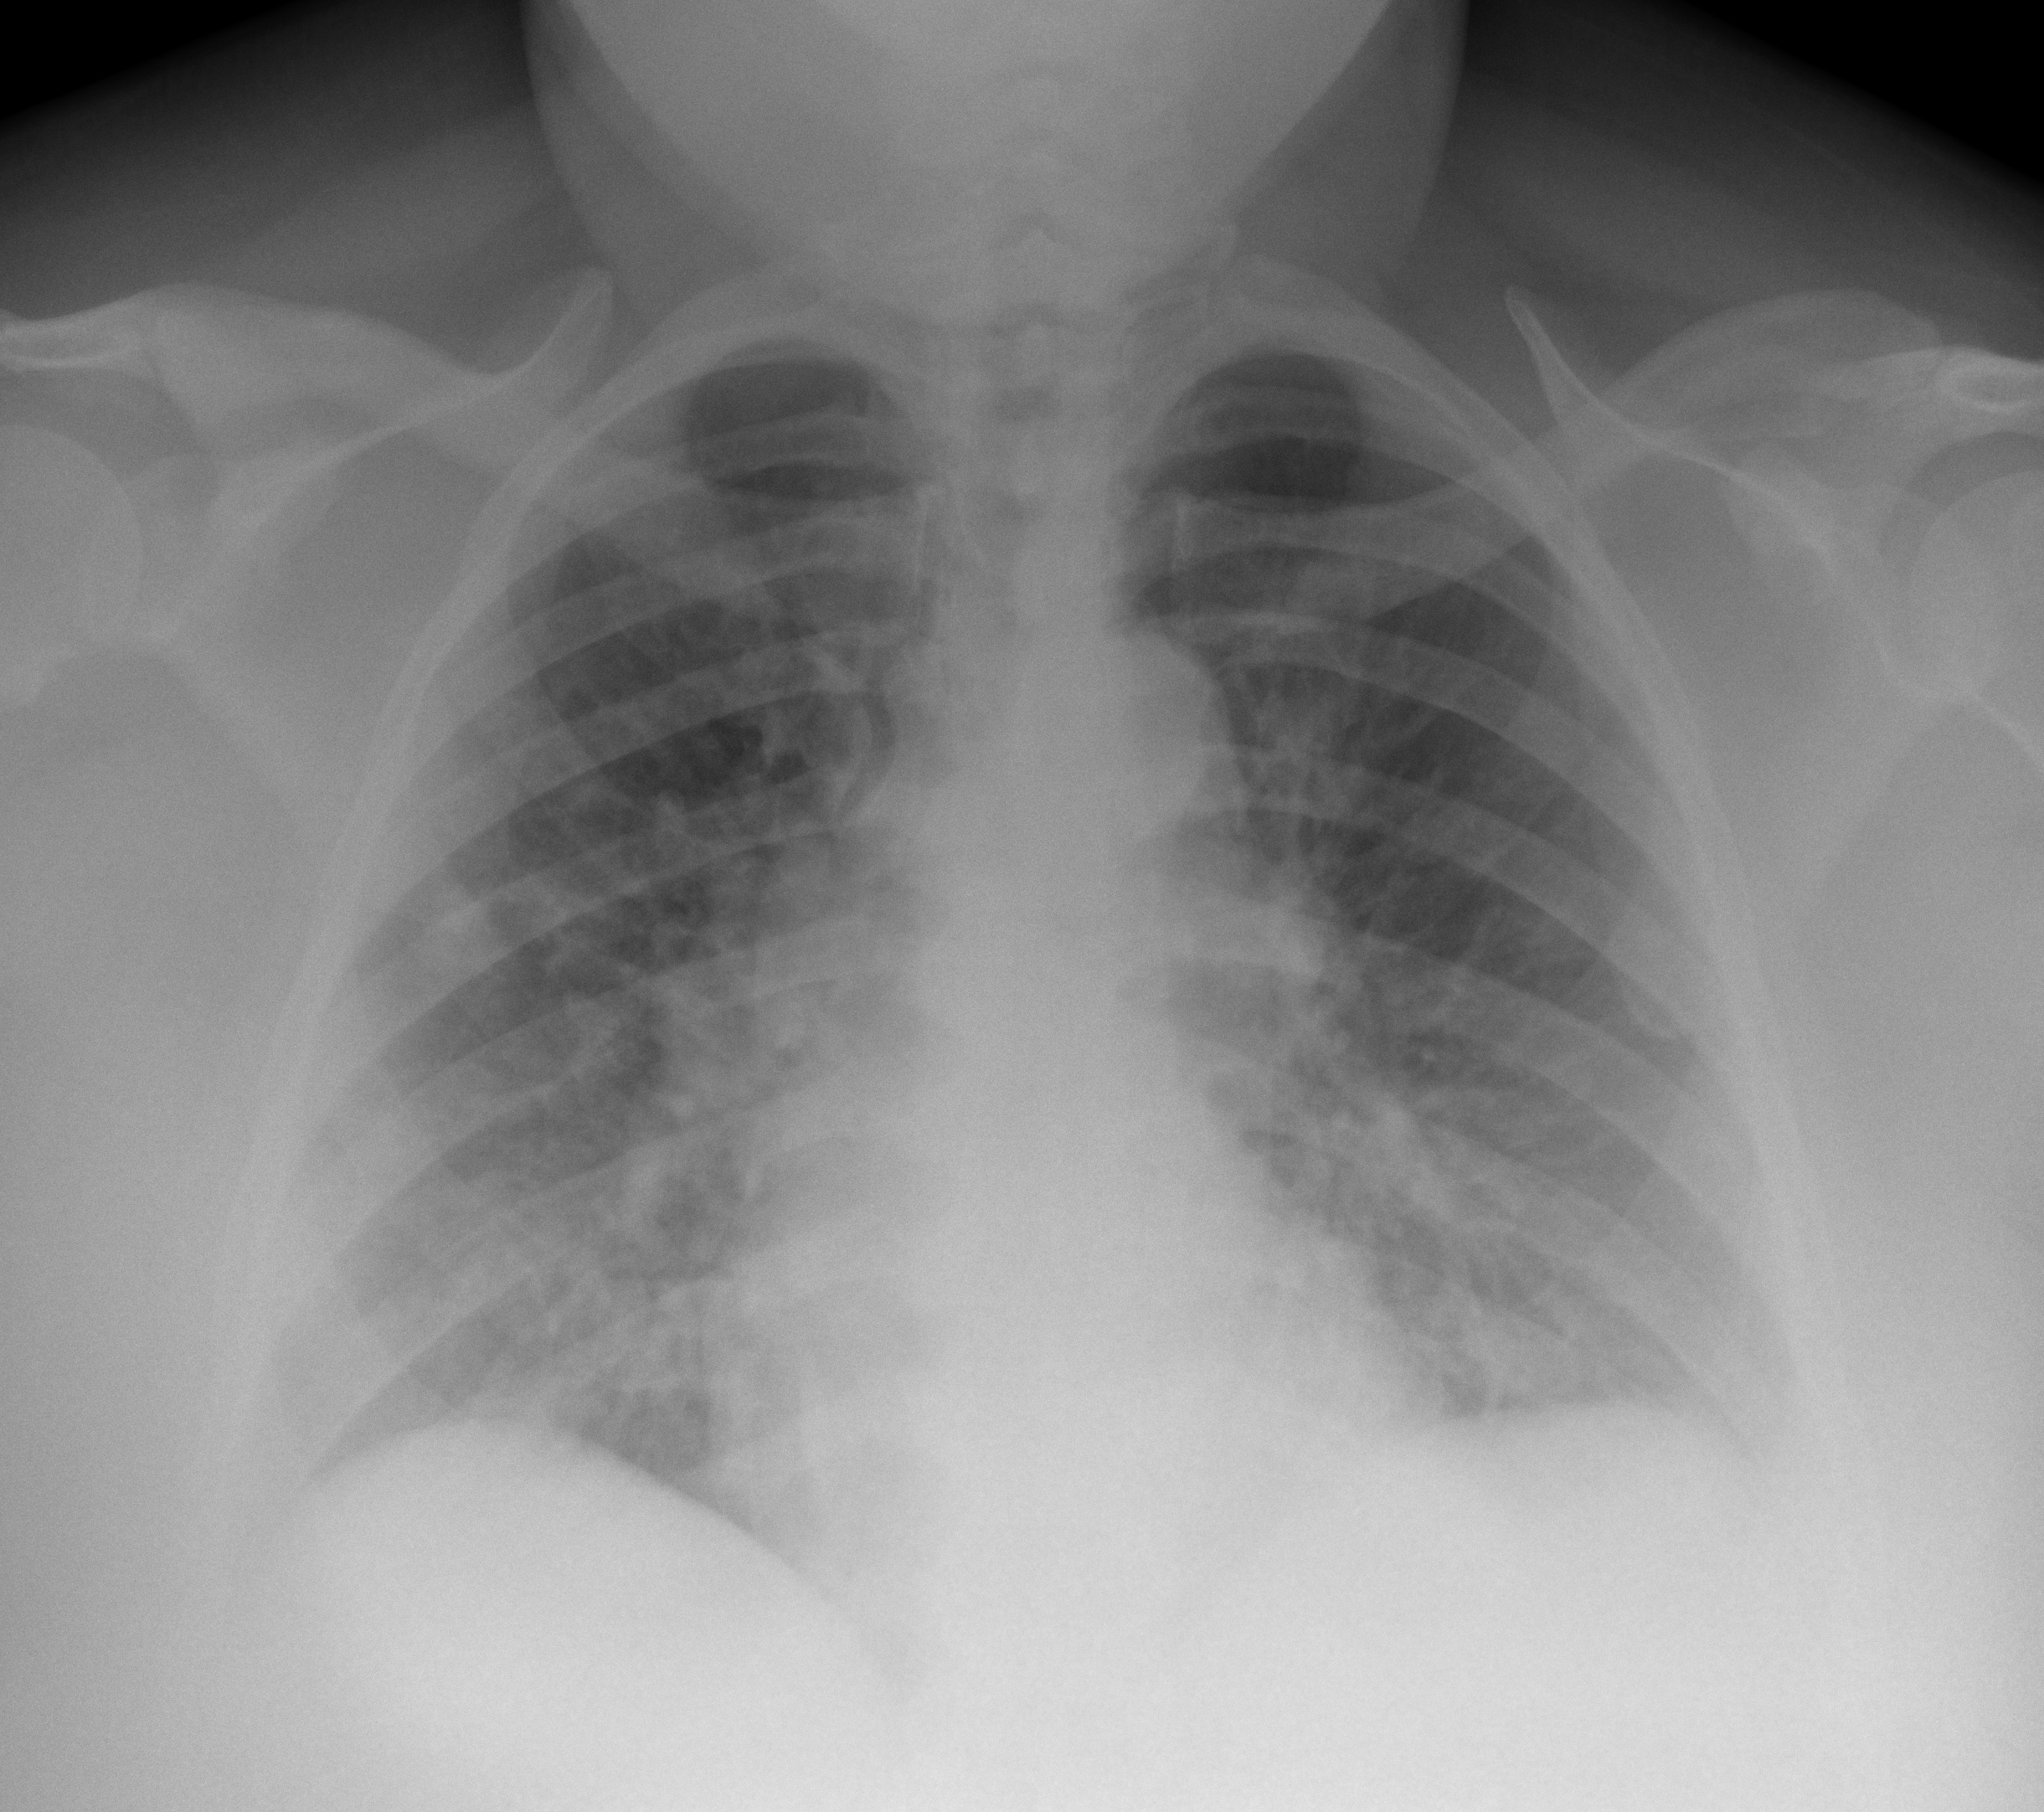
Chest X-ray (portable), AP projection. Female patient, age 49 years; imaged 10 days after the COVID-19 diagnosis.
Radiologist's key findings for this exam: There has been development of bilateral lower lobe airspace disease consistent with multilobar pneumonia.